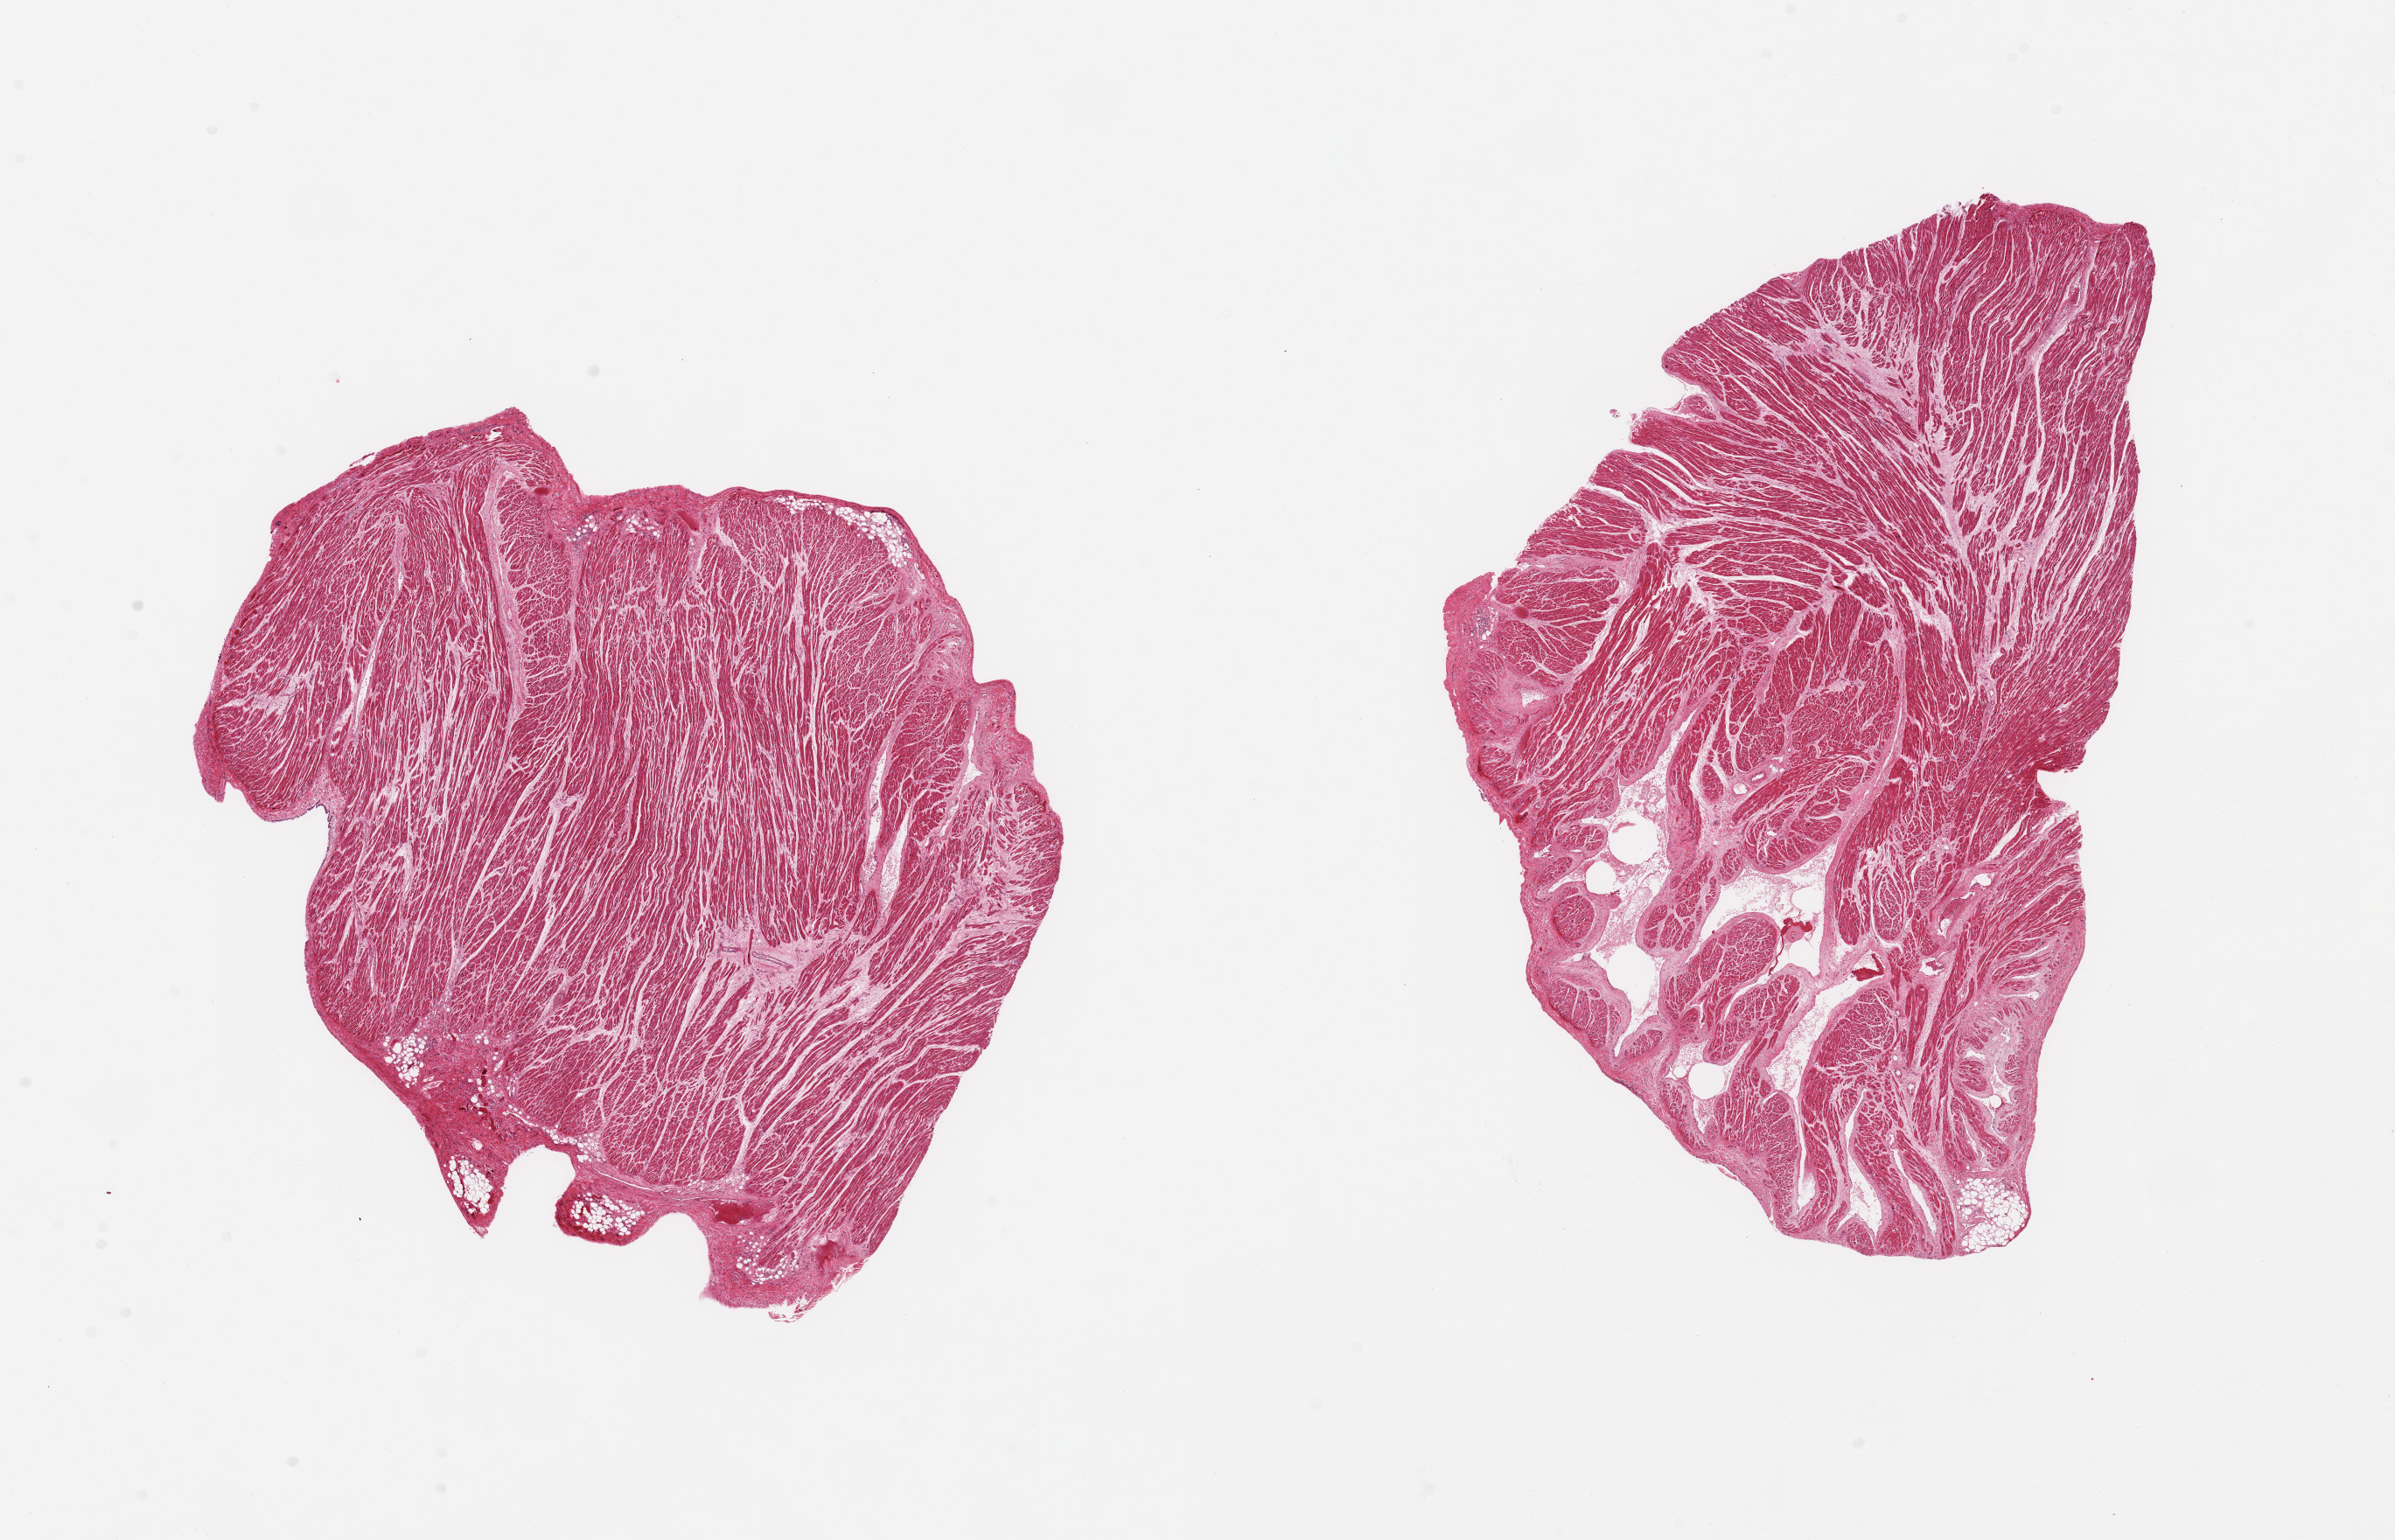
Whole-slide image, hematoxylin and eosin (H&E) stain — a low-resolution overview of the entire scanned area, about 21.7 x 13.9 mm (acquisition: 20x scan); PAXgene-fixed, paraffin-embedded tissue; section of auricular appendage (target tissue); donor tissue sample. Donor: male.
- reviewer comment on this tissue sample: 2 pieces; minimal extraneous tissue